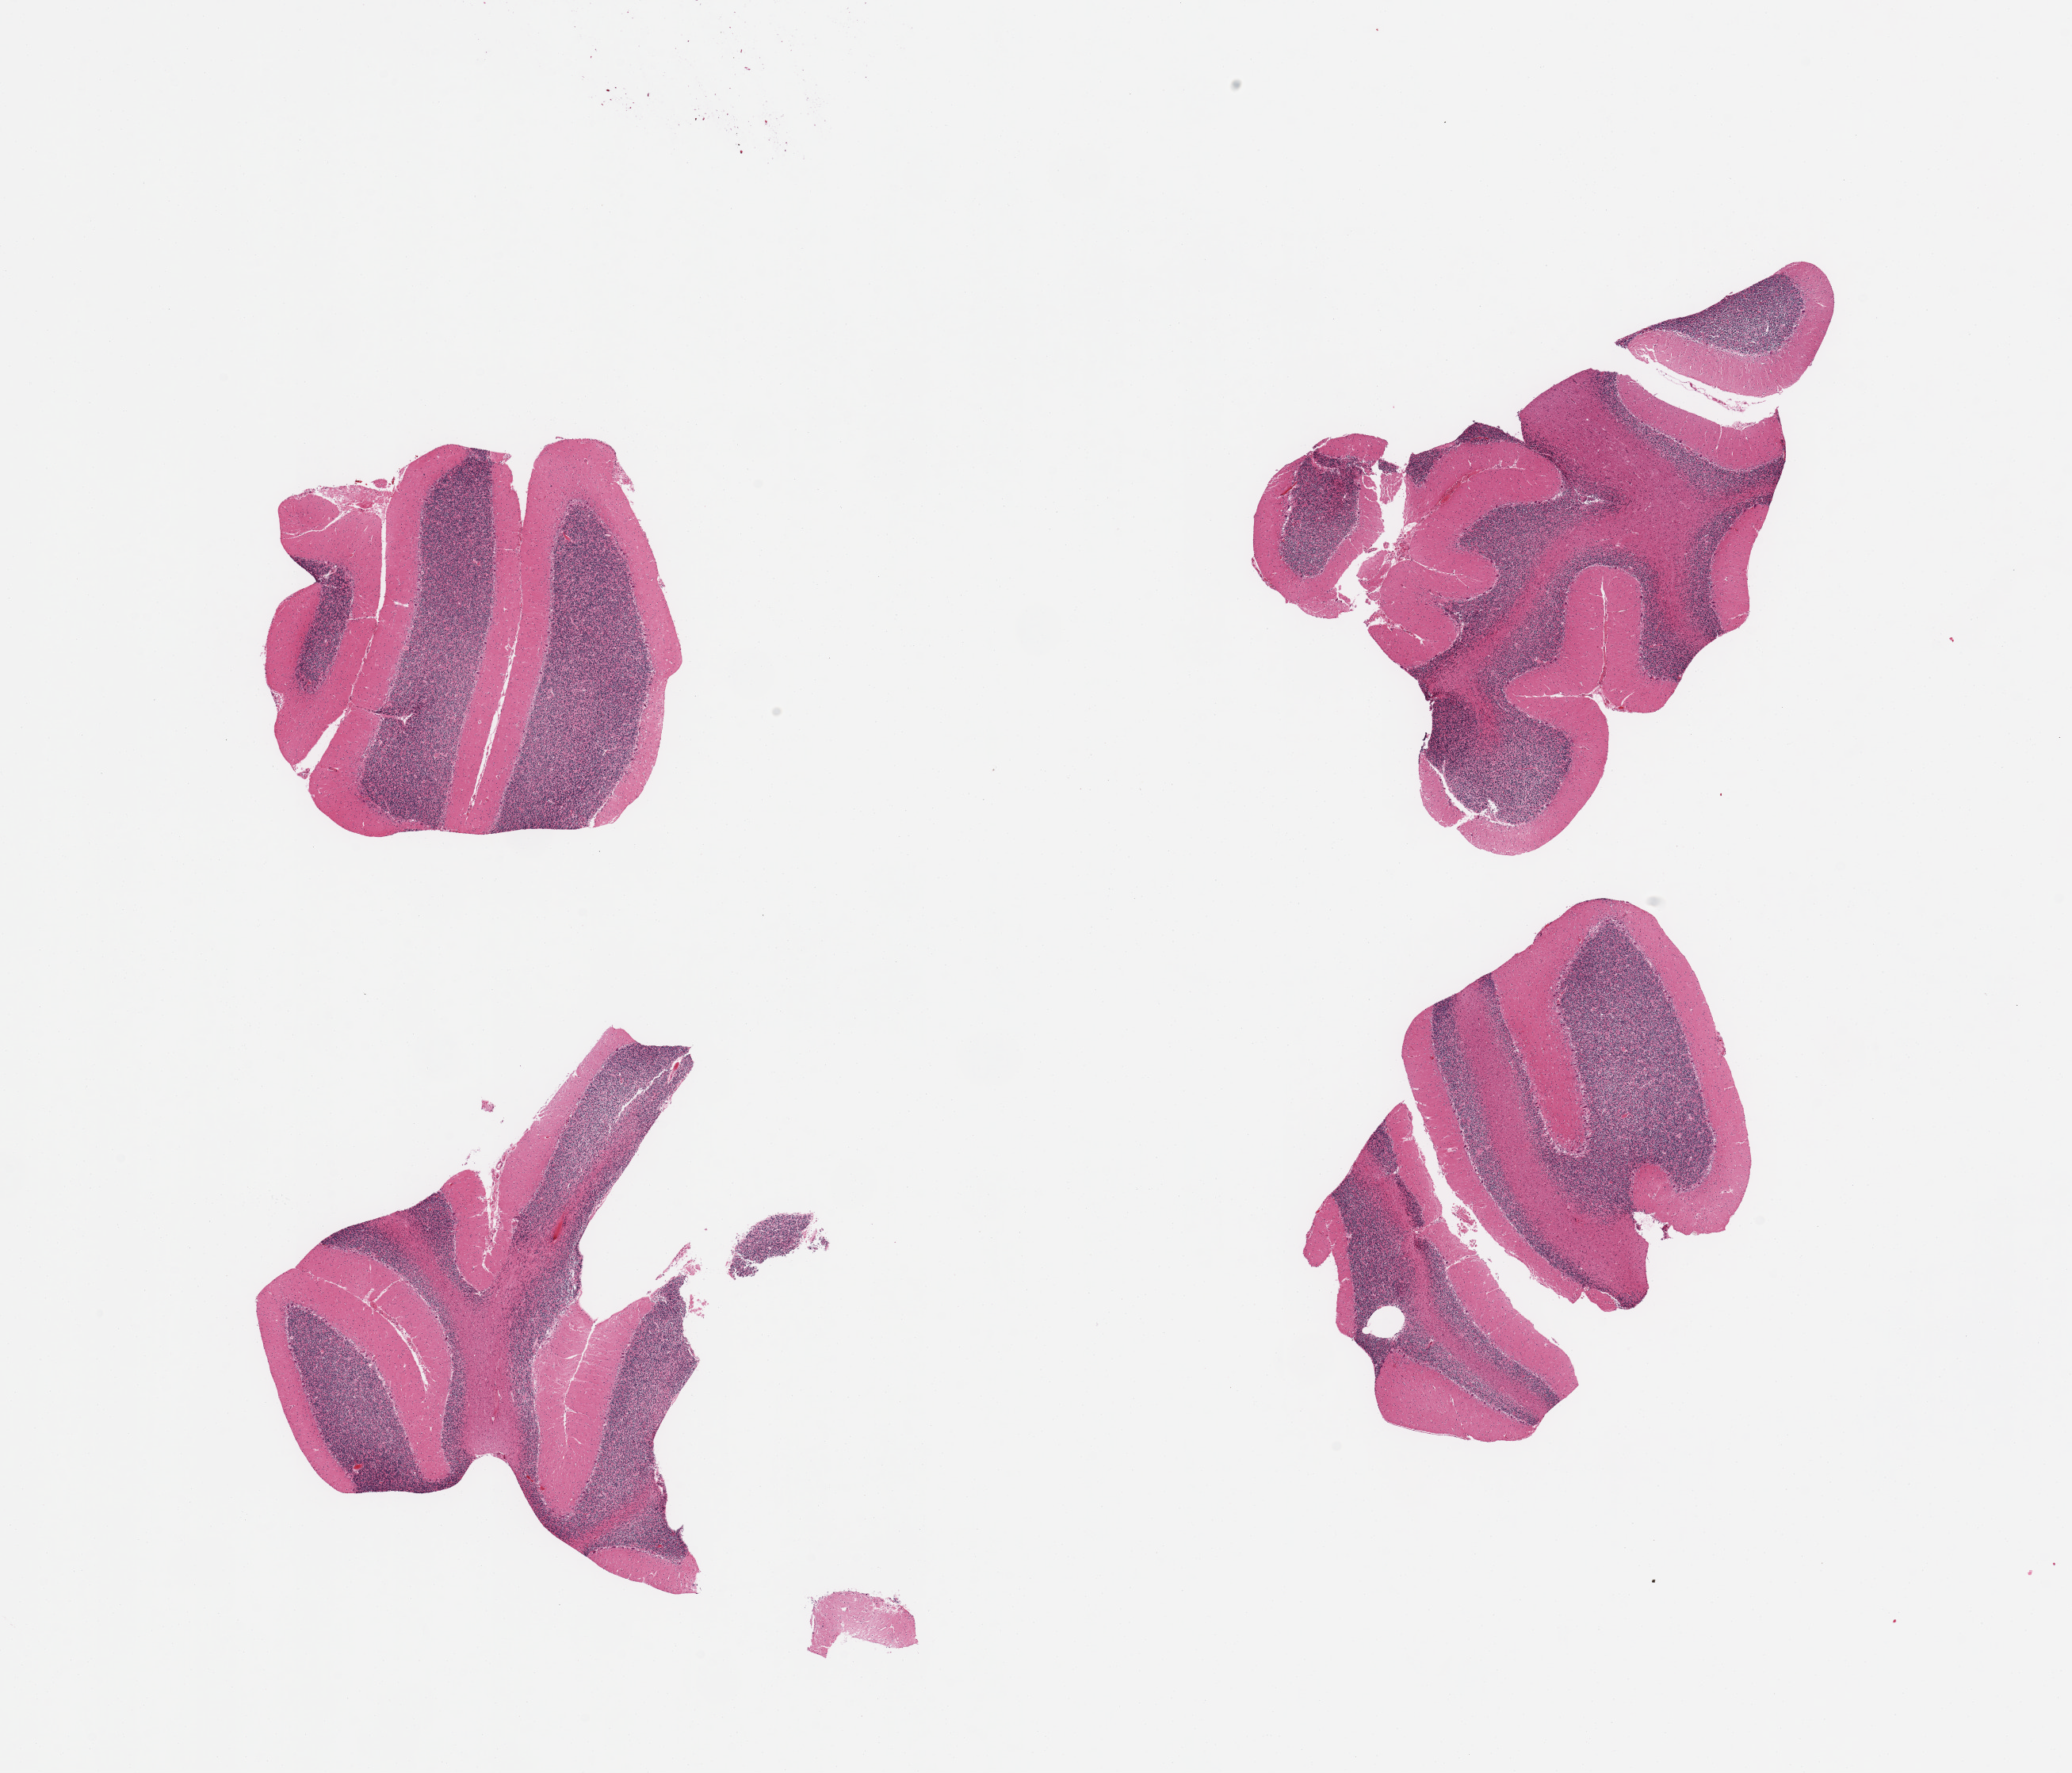
H&E whole-slide image, whole scanned area (about 20.7 x 17.7 mm, slide scanned at 20x) shown as a low-resolution overview. PAXgene-fixed paraffin-embedded (PFPE) section. Section of cerebellum (target tissue). Tissue donor sample. Donor: male.
- reviewer comment on this tissue sample: 4 pieces